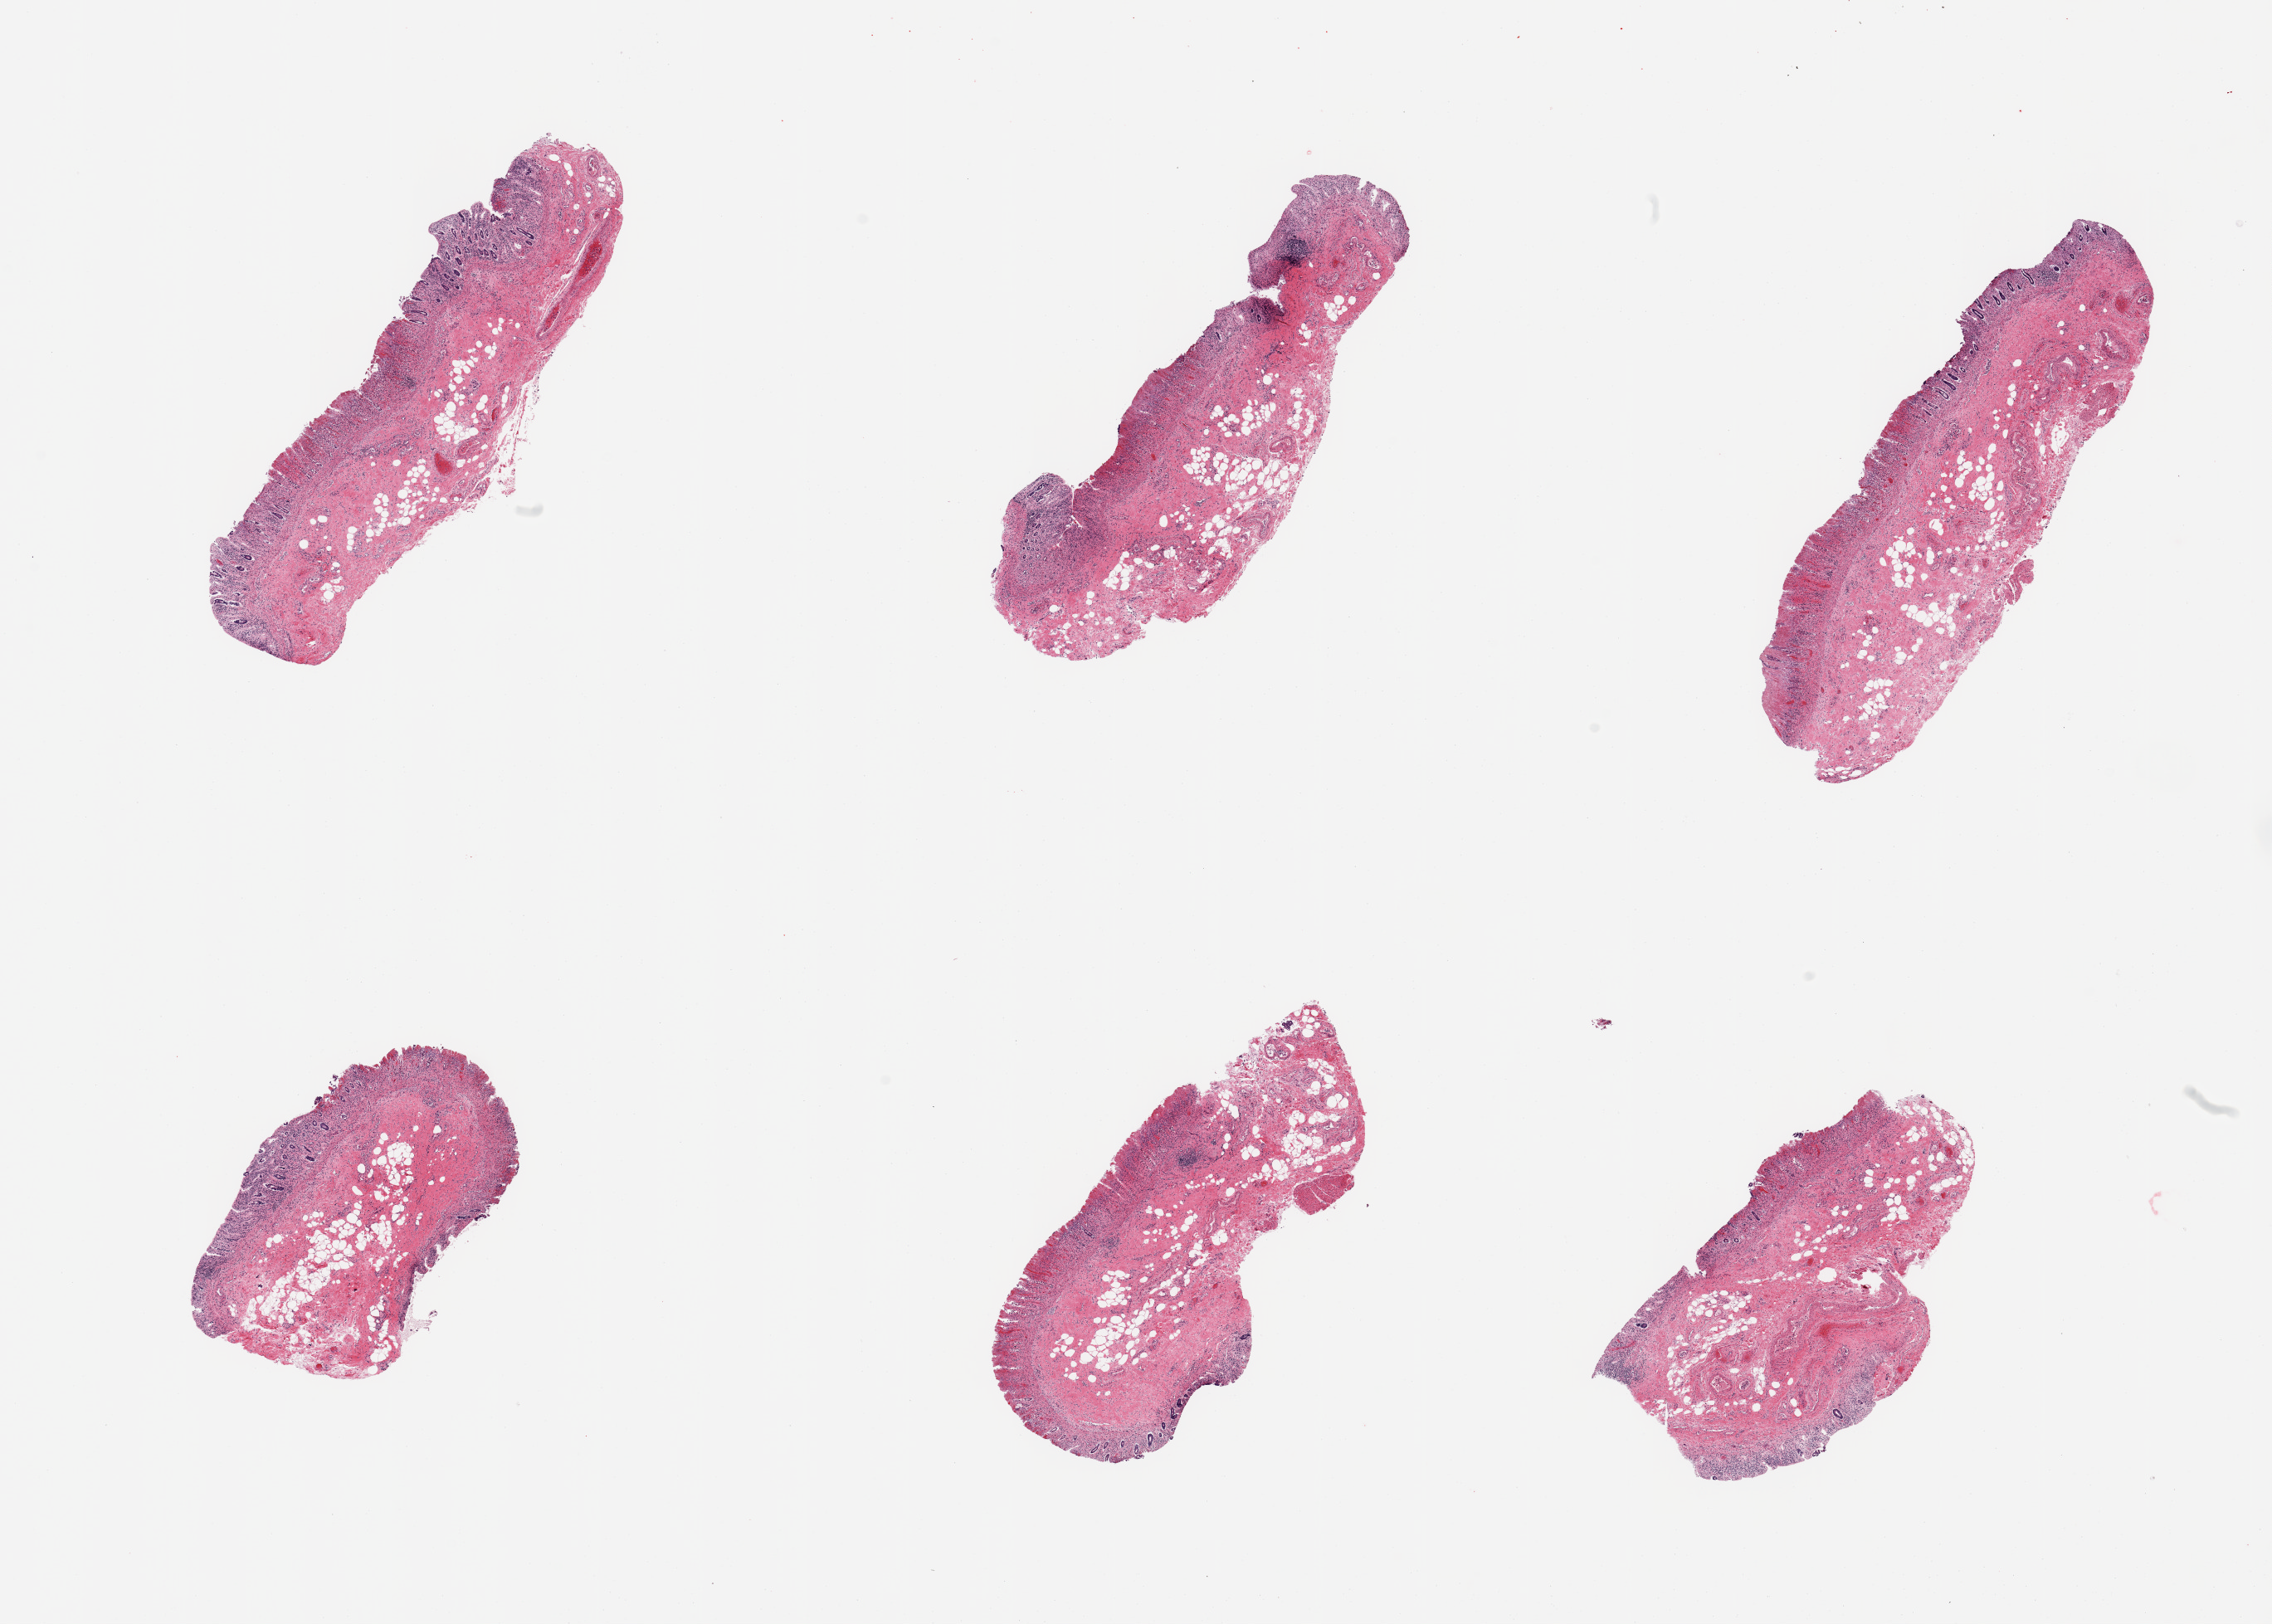
Whole-slide image, hematoxylin and eosin (H&E) stain — whole scanned area (about 21.7 x 15.5 mm) shown as a low-resolution overview. PAXgene-fixed, paraffin-embedded tissue. Section of transverse colon (target tissue). Donor tissue sample. Female donor.
Pathologist's review note for this sample: 6 pieces; mucosa autolyzed; muscularis not present.